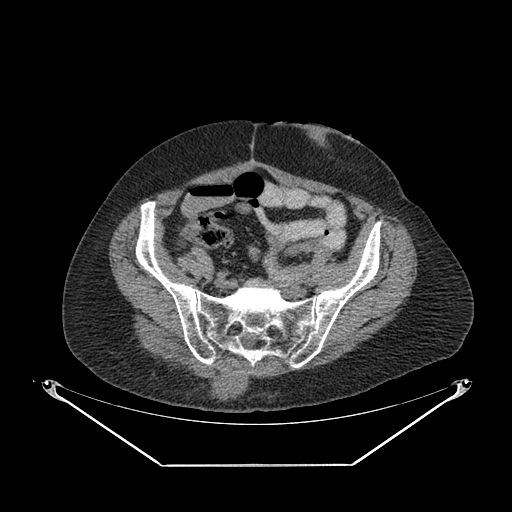
CT of an extremity soft-tissue mass (from a PET/CT study), one axial slice; slice 75 of 267 in the series (ordered by position); soft-tissue window (W 400 / L 40 HU); 3.75 mm slice thickness; 512 × 512 image matrix, field of view 500 × 500 mm. Female patient. From the clinical record (not read from this slice): histological type: spindle cell suggestive of myxofibrosarcoma; grade: intermediate; site of the primary tumour: right buttock.
Annotated regions visible in this slice (expert contour drawn on MRI and transferred to this co-registered scan by the dataset authors):
- gross tumour volume (mass): bounding box (x1, y1, x2, y2) in pixels: (151, 351, 250, 403)